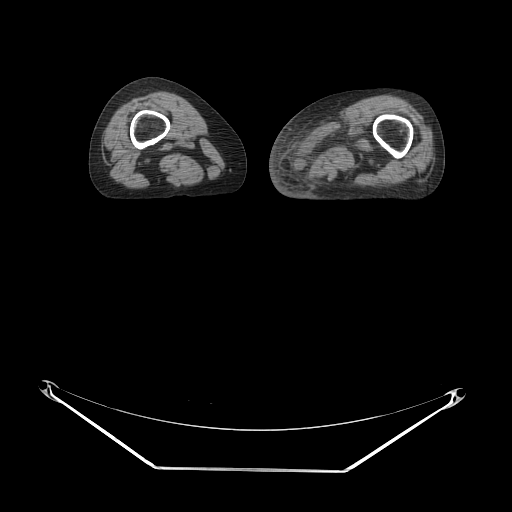
CT of an extremity soft-tissue mass (from a PET/CT study), one axial slice; slice 8 of 91 in the series (ordered by position); reconstruction kernel STANDARD; 140 kVp; soft-tissue window (W 400 / L 40 HU); 3.75 mm slice thickness; 512 × 512 image matrix, field of view 500 × 500 mm. Female patient. From the clinical record (not read from this slice): histological type: pleomorphic leiomyosarcoma; grade: high; site of the primary tumour: left thigh.
Annotated regions visible in this slice (expert contour drawn on MRI and transferred to this co-registered scan by the dataset authors):
- gross tumour volume including surrounding oedema: bounding box (x1, y1, x2, y2) in pixels: (302, 112, 382, 177)